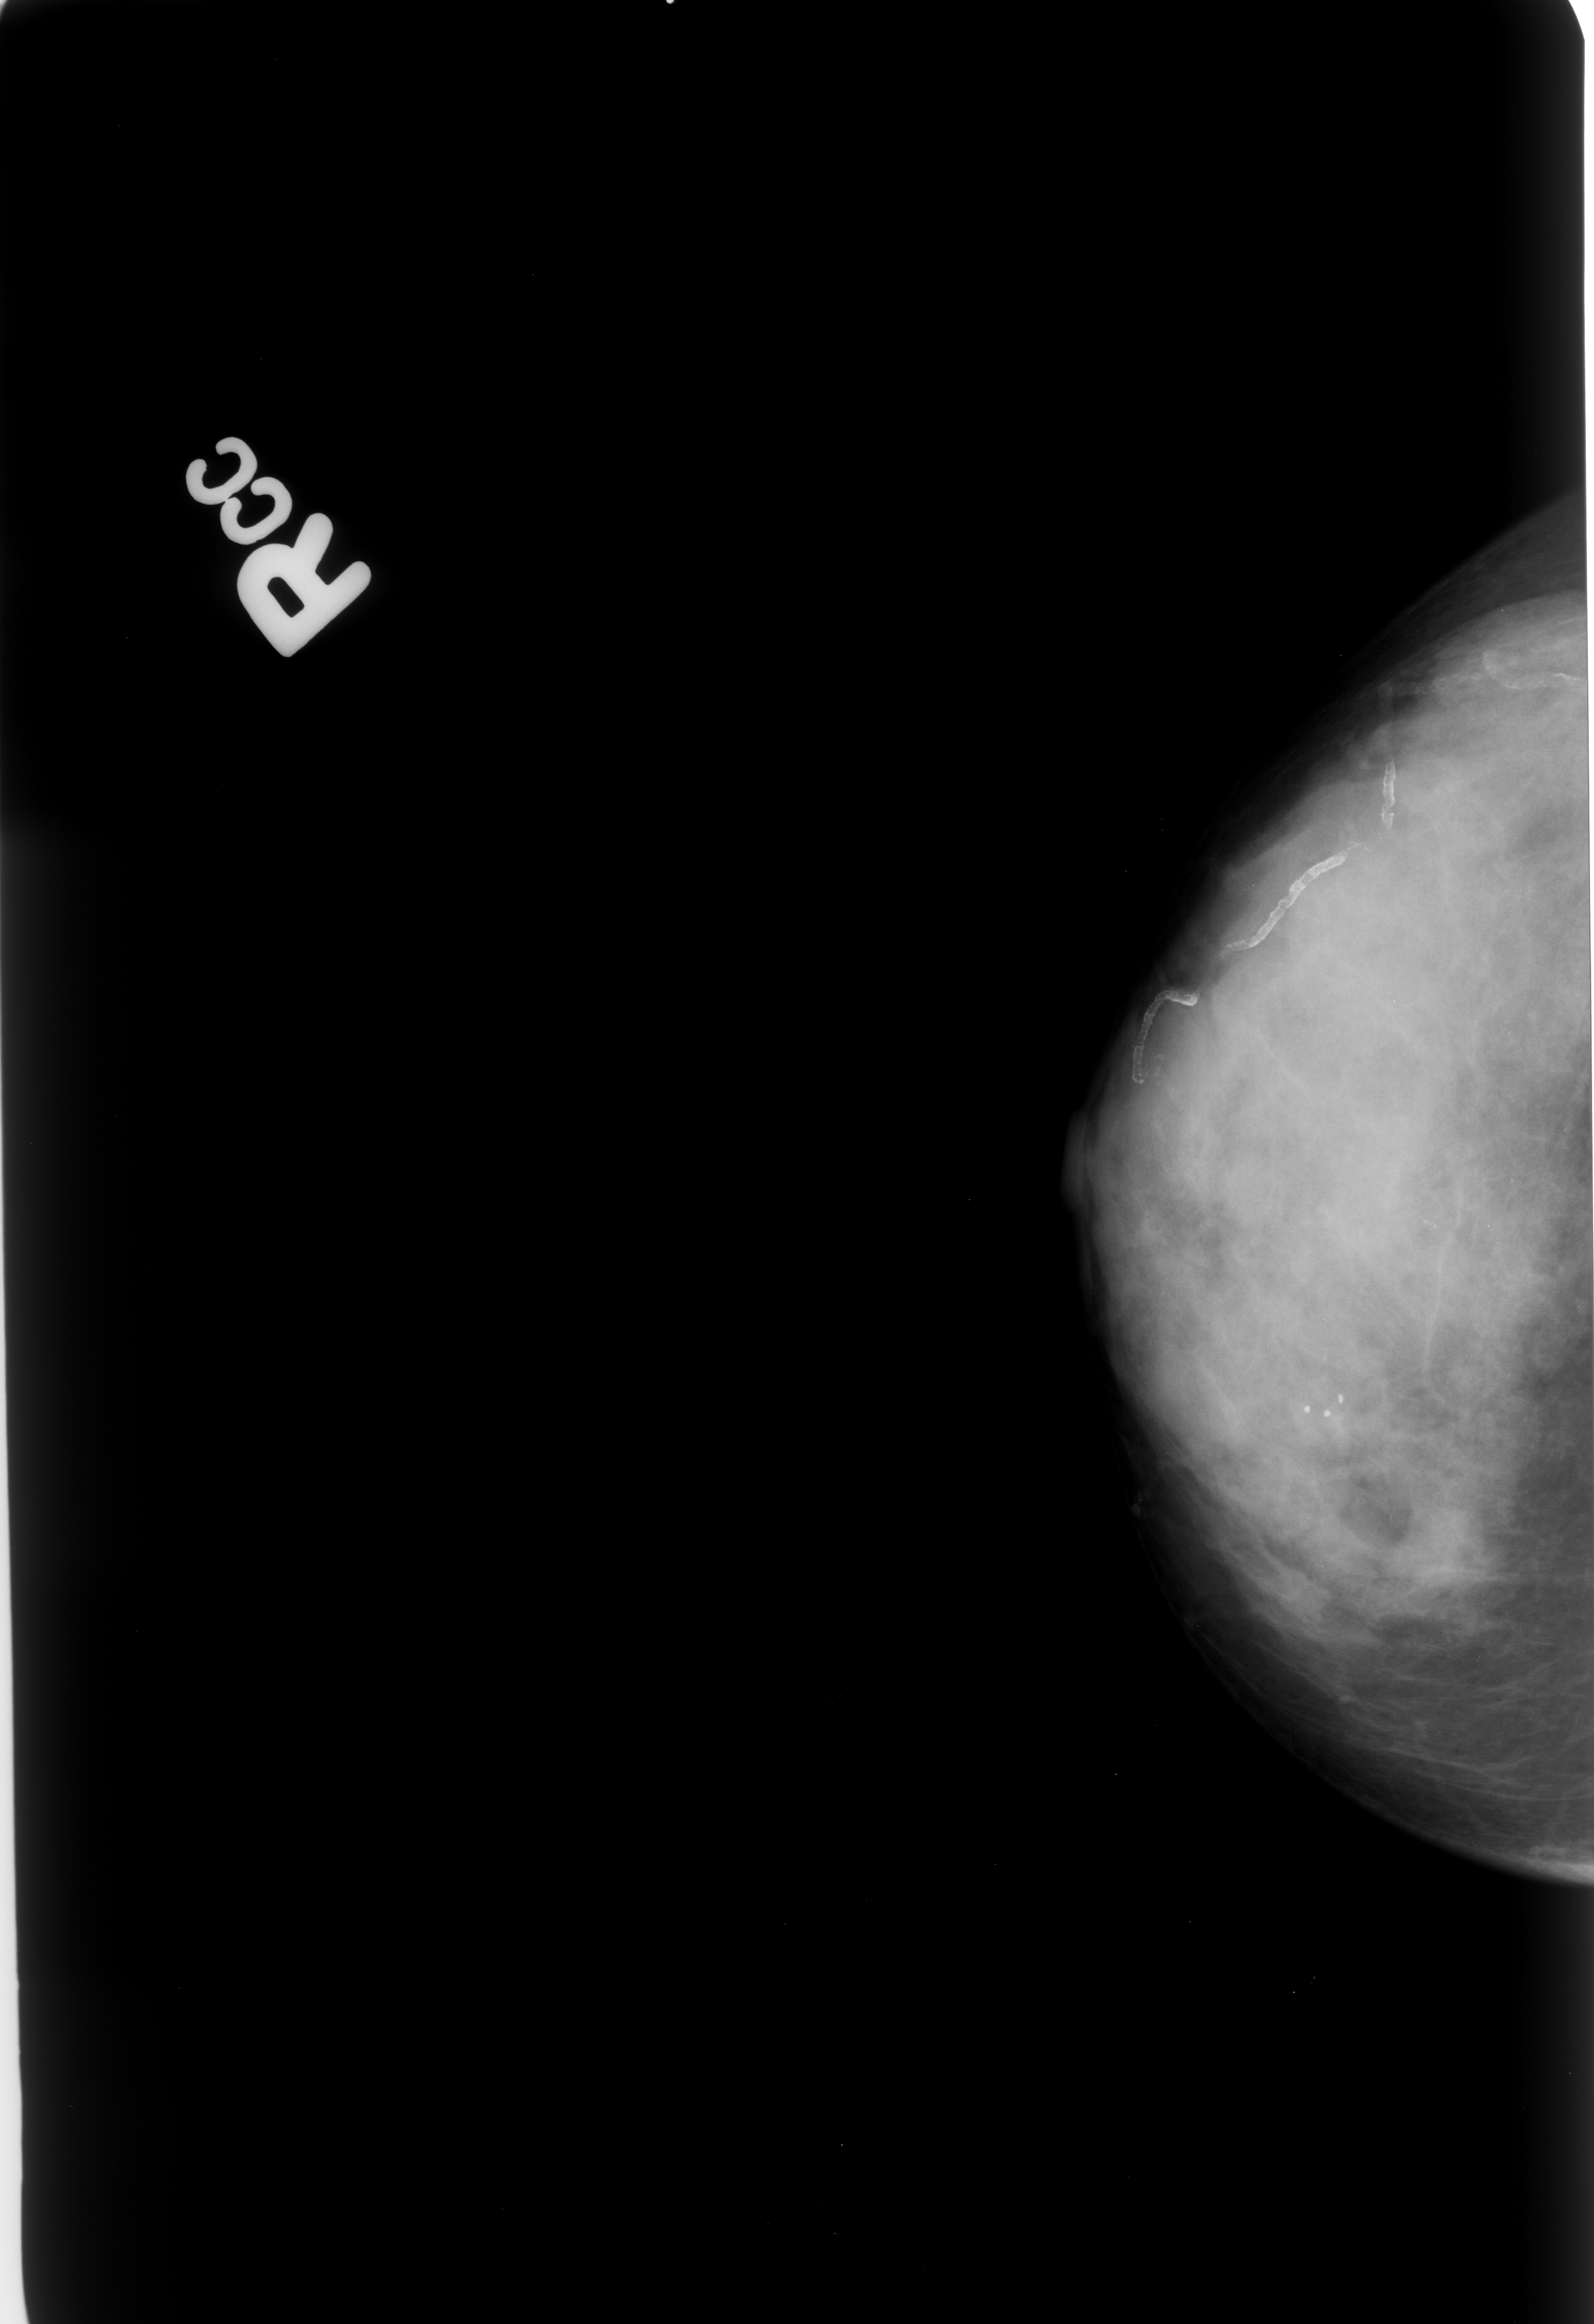
Scanned film-screen mammogram; right breast; craniocaudal (CC) view; 1594 × 2324 image matrix.
Marked abnormalities (boxes around the expert regions of interest):
- calcifications, morphology pleomorphic, distribution clustered; BI-RADS assessment category 4; subtlety rating 3 on a 1 (subtle) to 5 (obvious) scale; pathology (as recorded): benign: box from (x=1375, y=1195) to (x=1461, y=1285) px